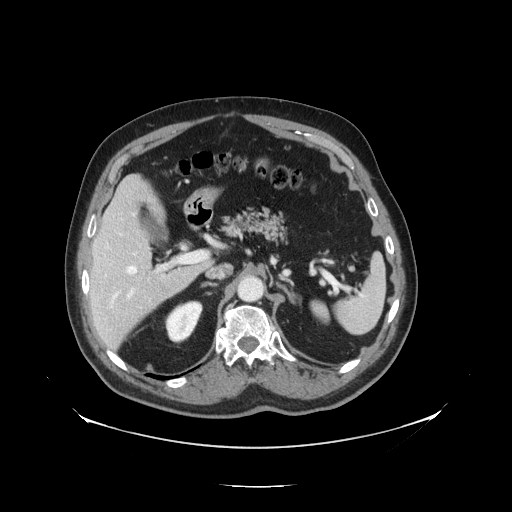
Contrast-enhanced abdominal CT, one axial slice; position 83 of 138 along the scan axis; 120 kVp; intravenous contrast given; soft-tissue window (W 400 / L 40 HU); 2.5 mm slice thickness; 512 × 512 image matrix, field of view 497 × 497 mm. Male patient, age 77 years. Case-level facts recorded for this patient, not image findings: diagnosis: colorectal cancer liver metastases, imaged before liver resection; multiple liver metastases: no; largest metastasis: 1.5 cm; chemotherapy before resection: no.
Annotated regions visible in this slice (expert manual segmentation):
- hepatic veins: box from (x=126, y=266) to (x=137, y=274) px
- liver: (x=90, y=177)–(x=211, y=350)
- planned liver remnant (the part of the liver to remain after resection): (x=91, y=177)–(x=166, y=287)
- portal vein (with intrahepatic branches): (x=126, y=253)–(x=205, y=300)
- liver metastasis: (x=160, y=282)–(x=166, y=289)